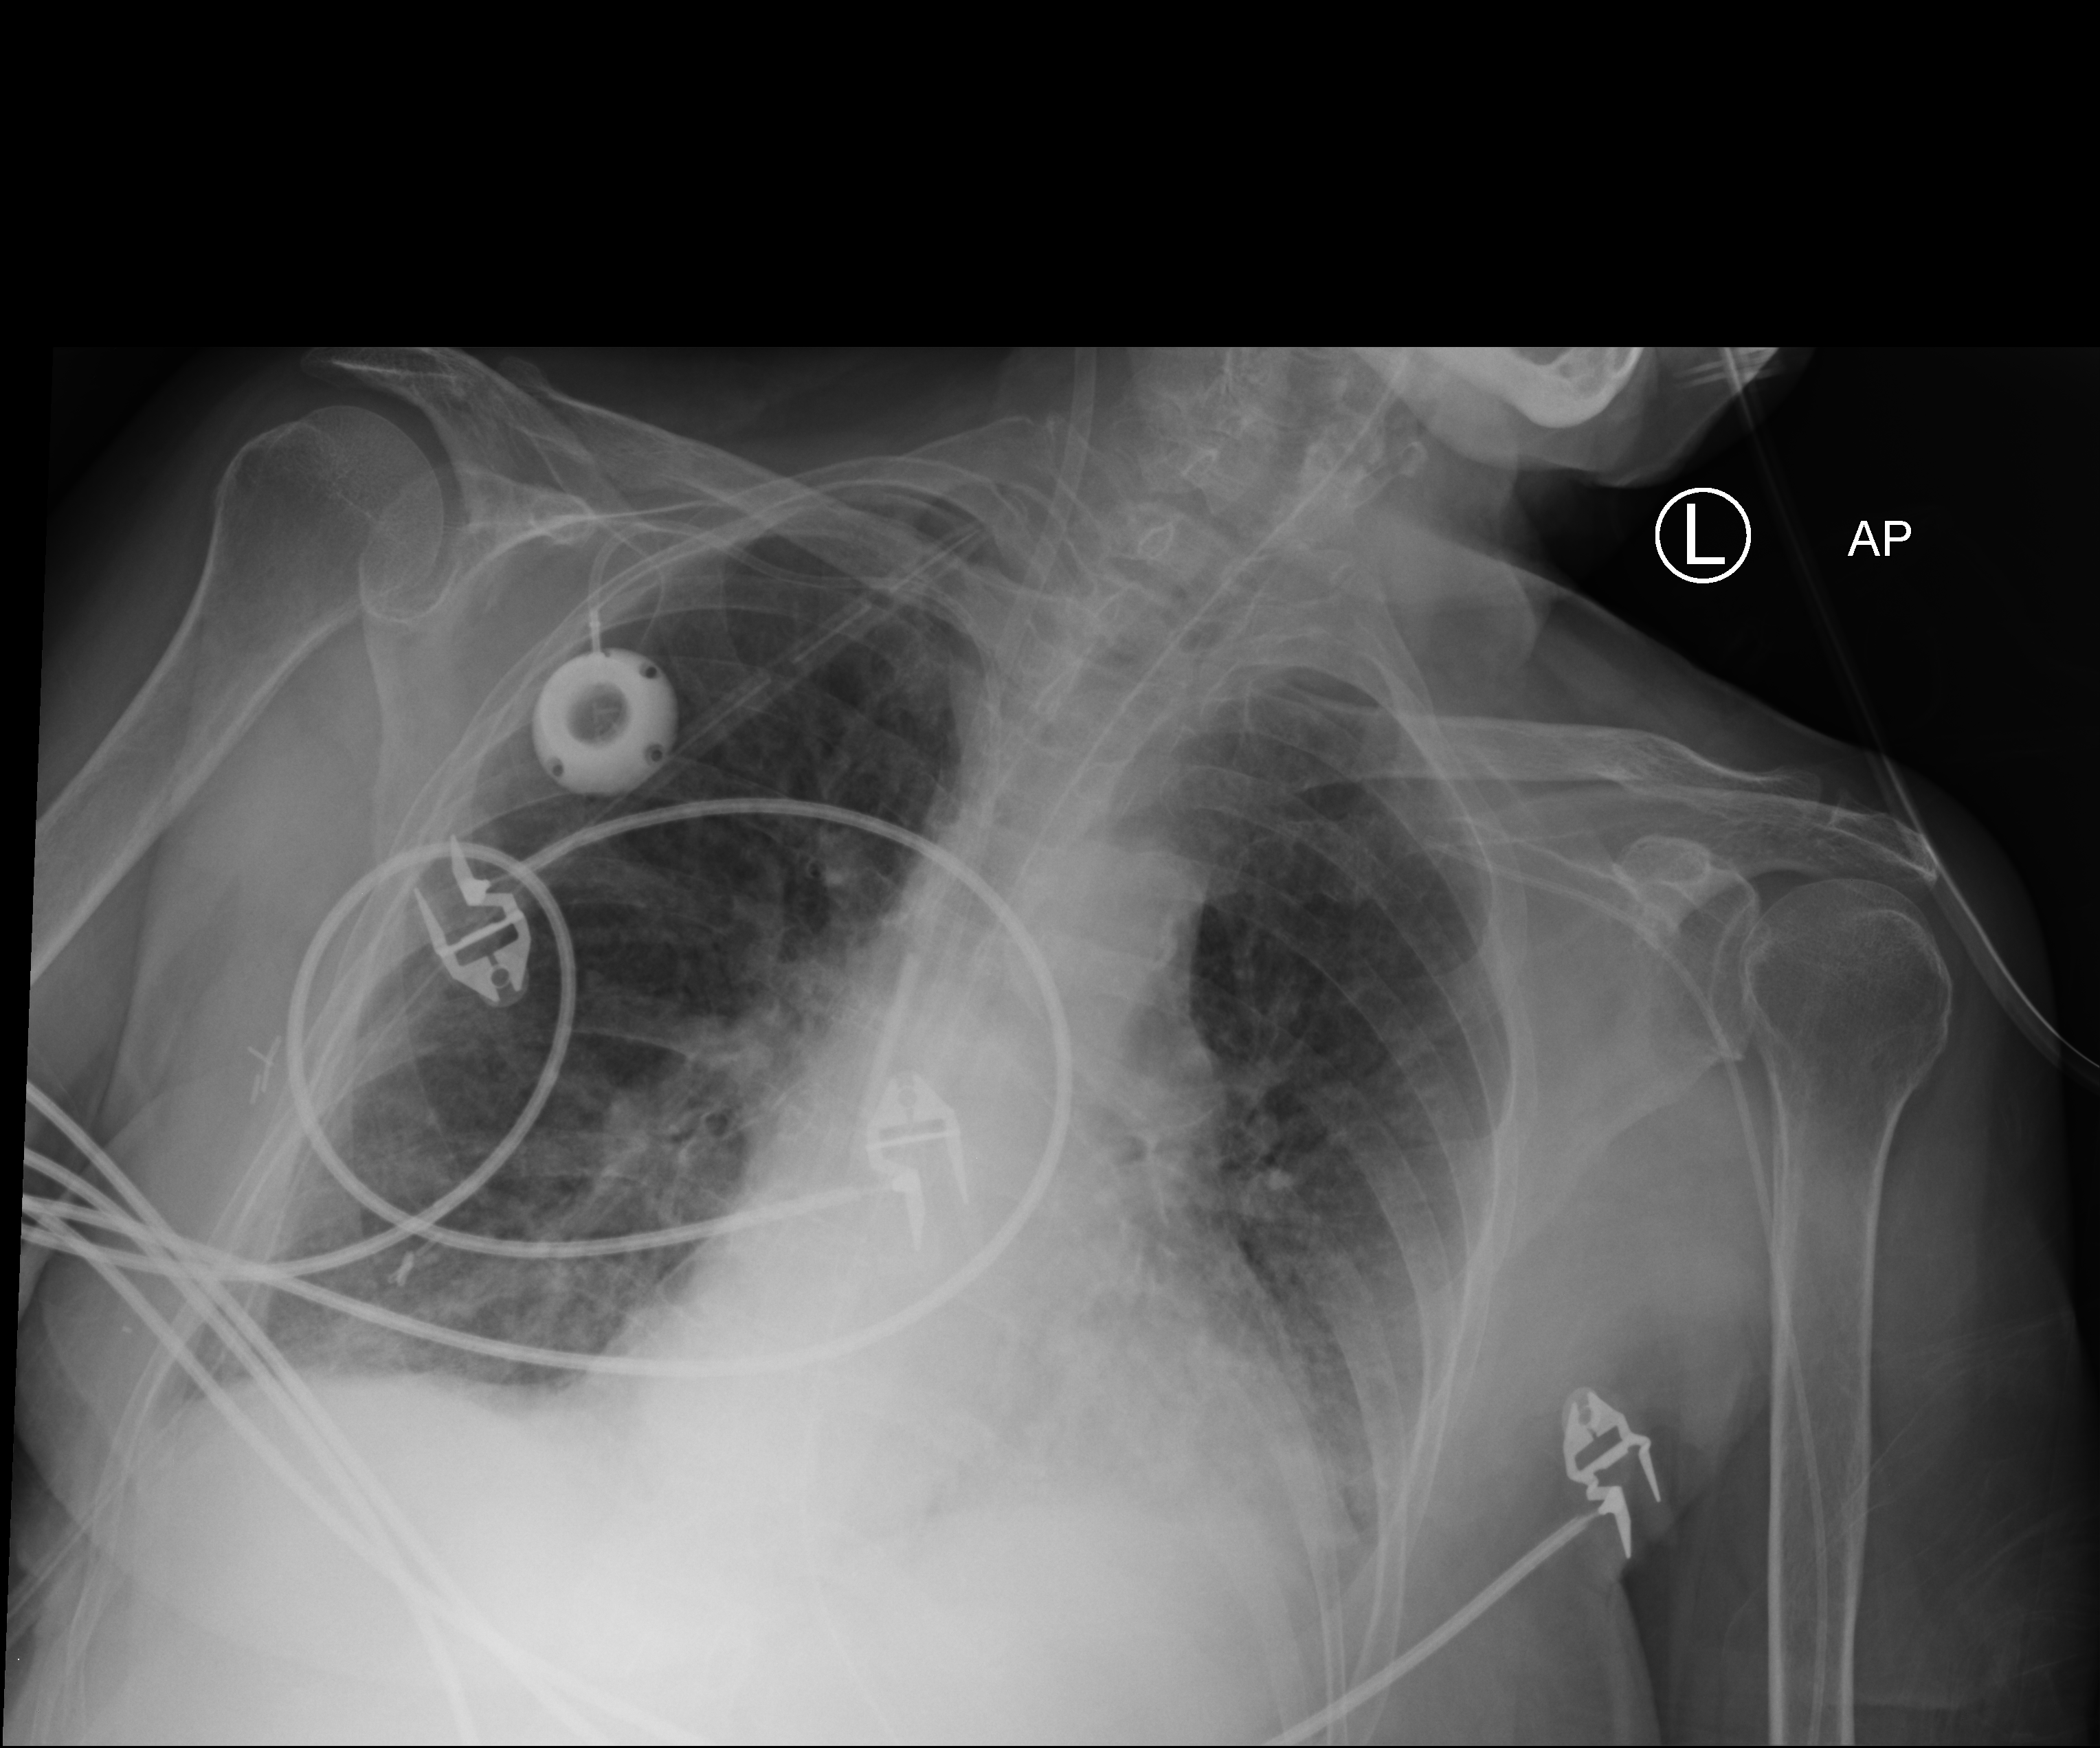
Bedside chest radiograph (computed radiography), anteroposterior (AP) projection. Patient hospitalised with COVID-19; female, aged 60–74 years.
Hospital-stay facts (about this admission, not read from this image; timing relative to this image not recorded):
- admitted to intensive care during this hospital stay: yes